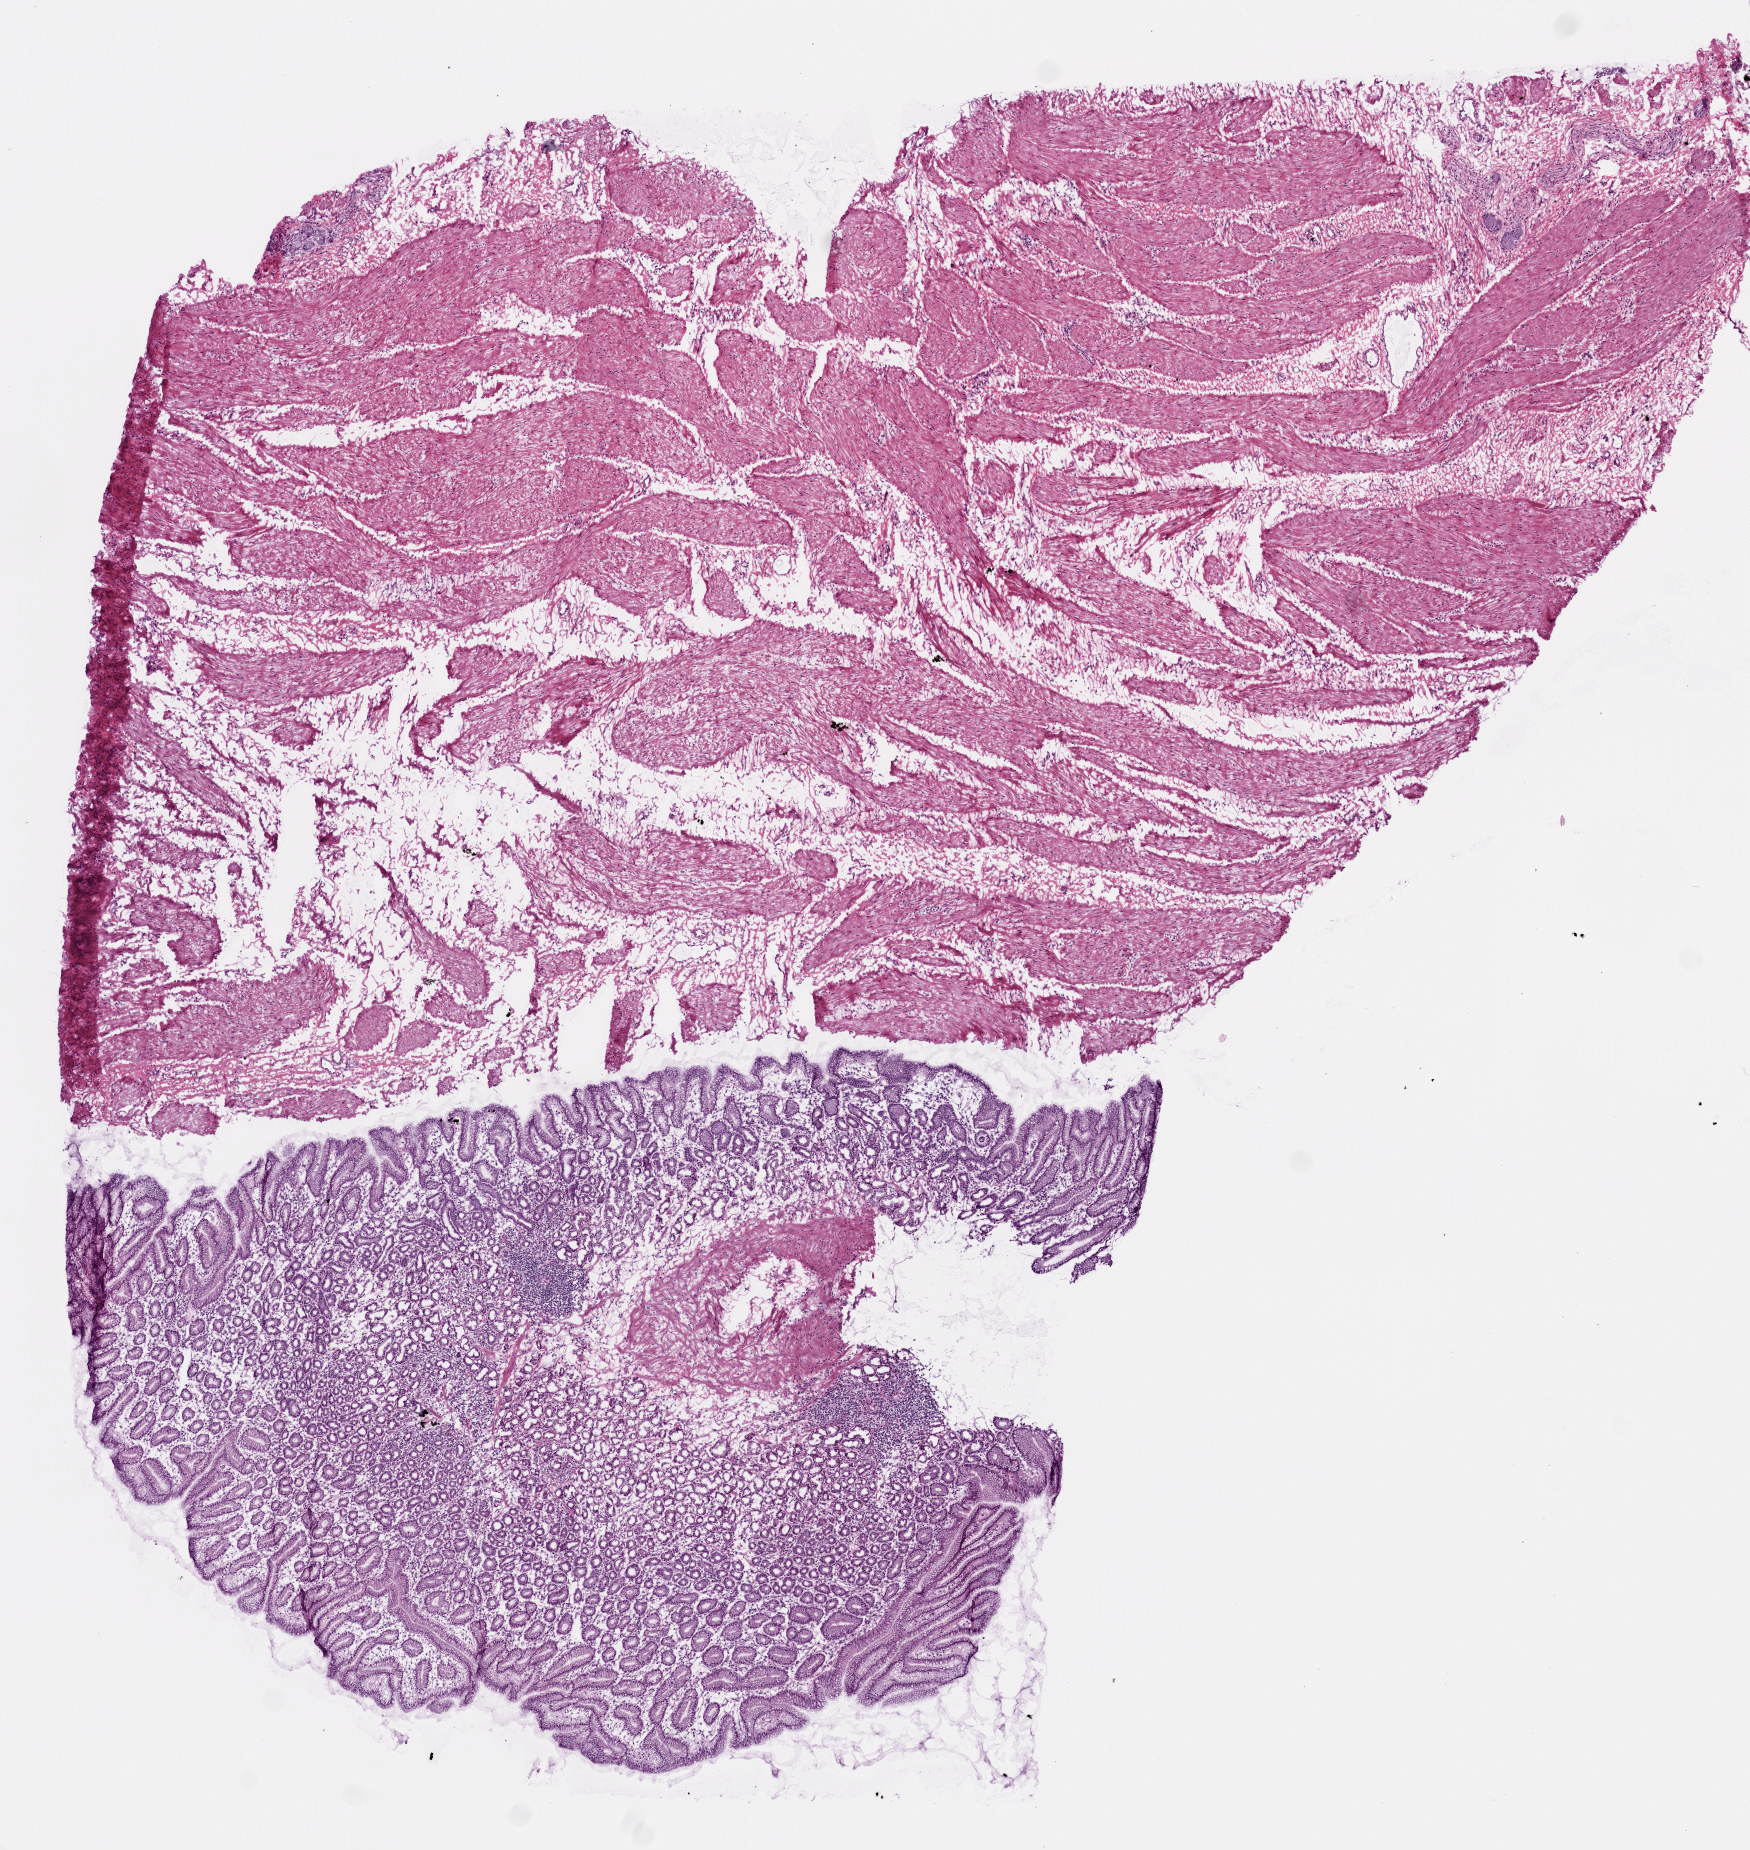
Digitized Hematoxylin and eosin (H&E) stained tissue section (whole slide), a low-resolution overview of the entire scanned area, about 7.0 x 7.4 mm (slide scanned at 20x). Frozen section from the top of the tissue portion. Sample: solid tissue normal (non-tumour tissue), stomach. Male, age 72 years at initial diagnosis.
• this section: solid tissue normal (non-tumour) sample from the same patient
• patient diagnosis: Adenocarcinoma, NOS (cardia, NOS)